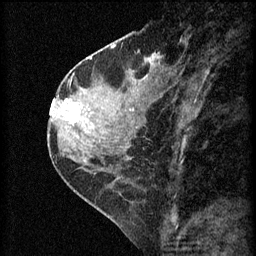
Breast MRI (dynamic contrast-enhanced), one sagittal slice; position 26 of 60 along the scan axis; 3 images stored at this slice position (order not interpretable as contrast timing); 1.5 T; TE 4.2 ms, TR 8.2 ms; 2 mm slice thickness; 256 × 256 image matrix, field of view 180 × 180 mm. Patient: female, 45 years.
Annotated regions visible in this slice (semi-automatic segmentation, software-assisted and operator-edited):
- analysis volume of interest (the breast-tissue region the enhancement analysis was run in; not a lesion): box from (x=62, y=98) to (x=104, y=139) px
- tumour enhancement mask (voxels above the 70 % enhancement threshold inside the analysis volume of interest): (x=63, y=98)–(x=81, y=123)